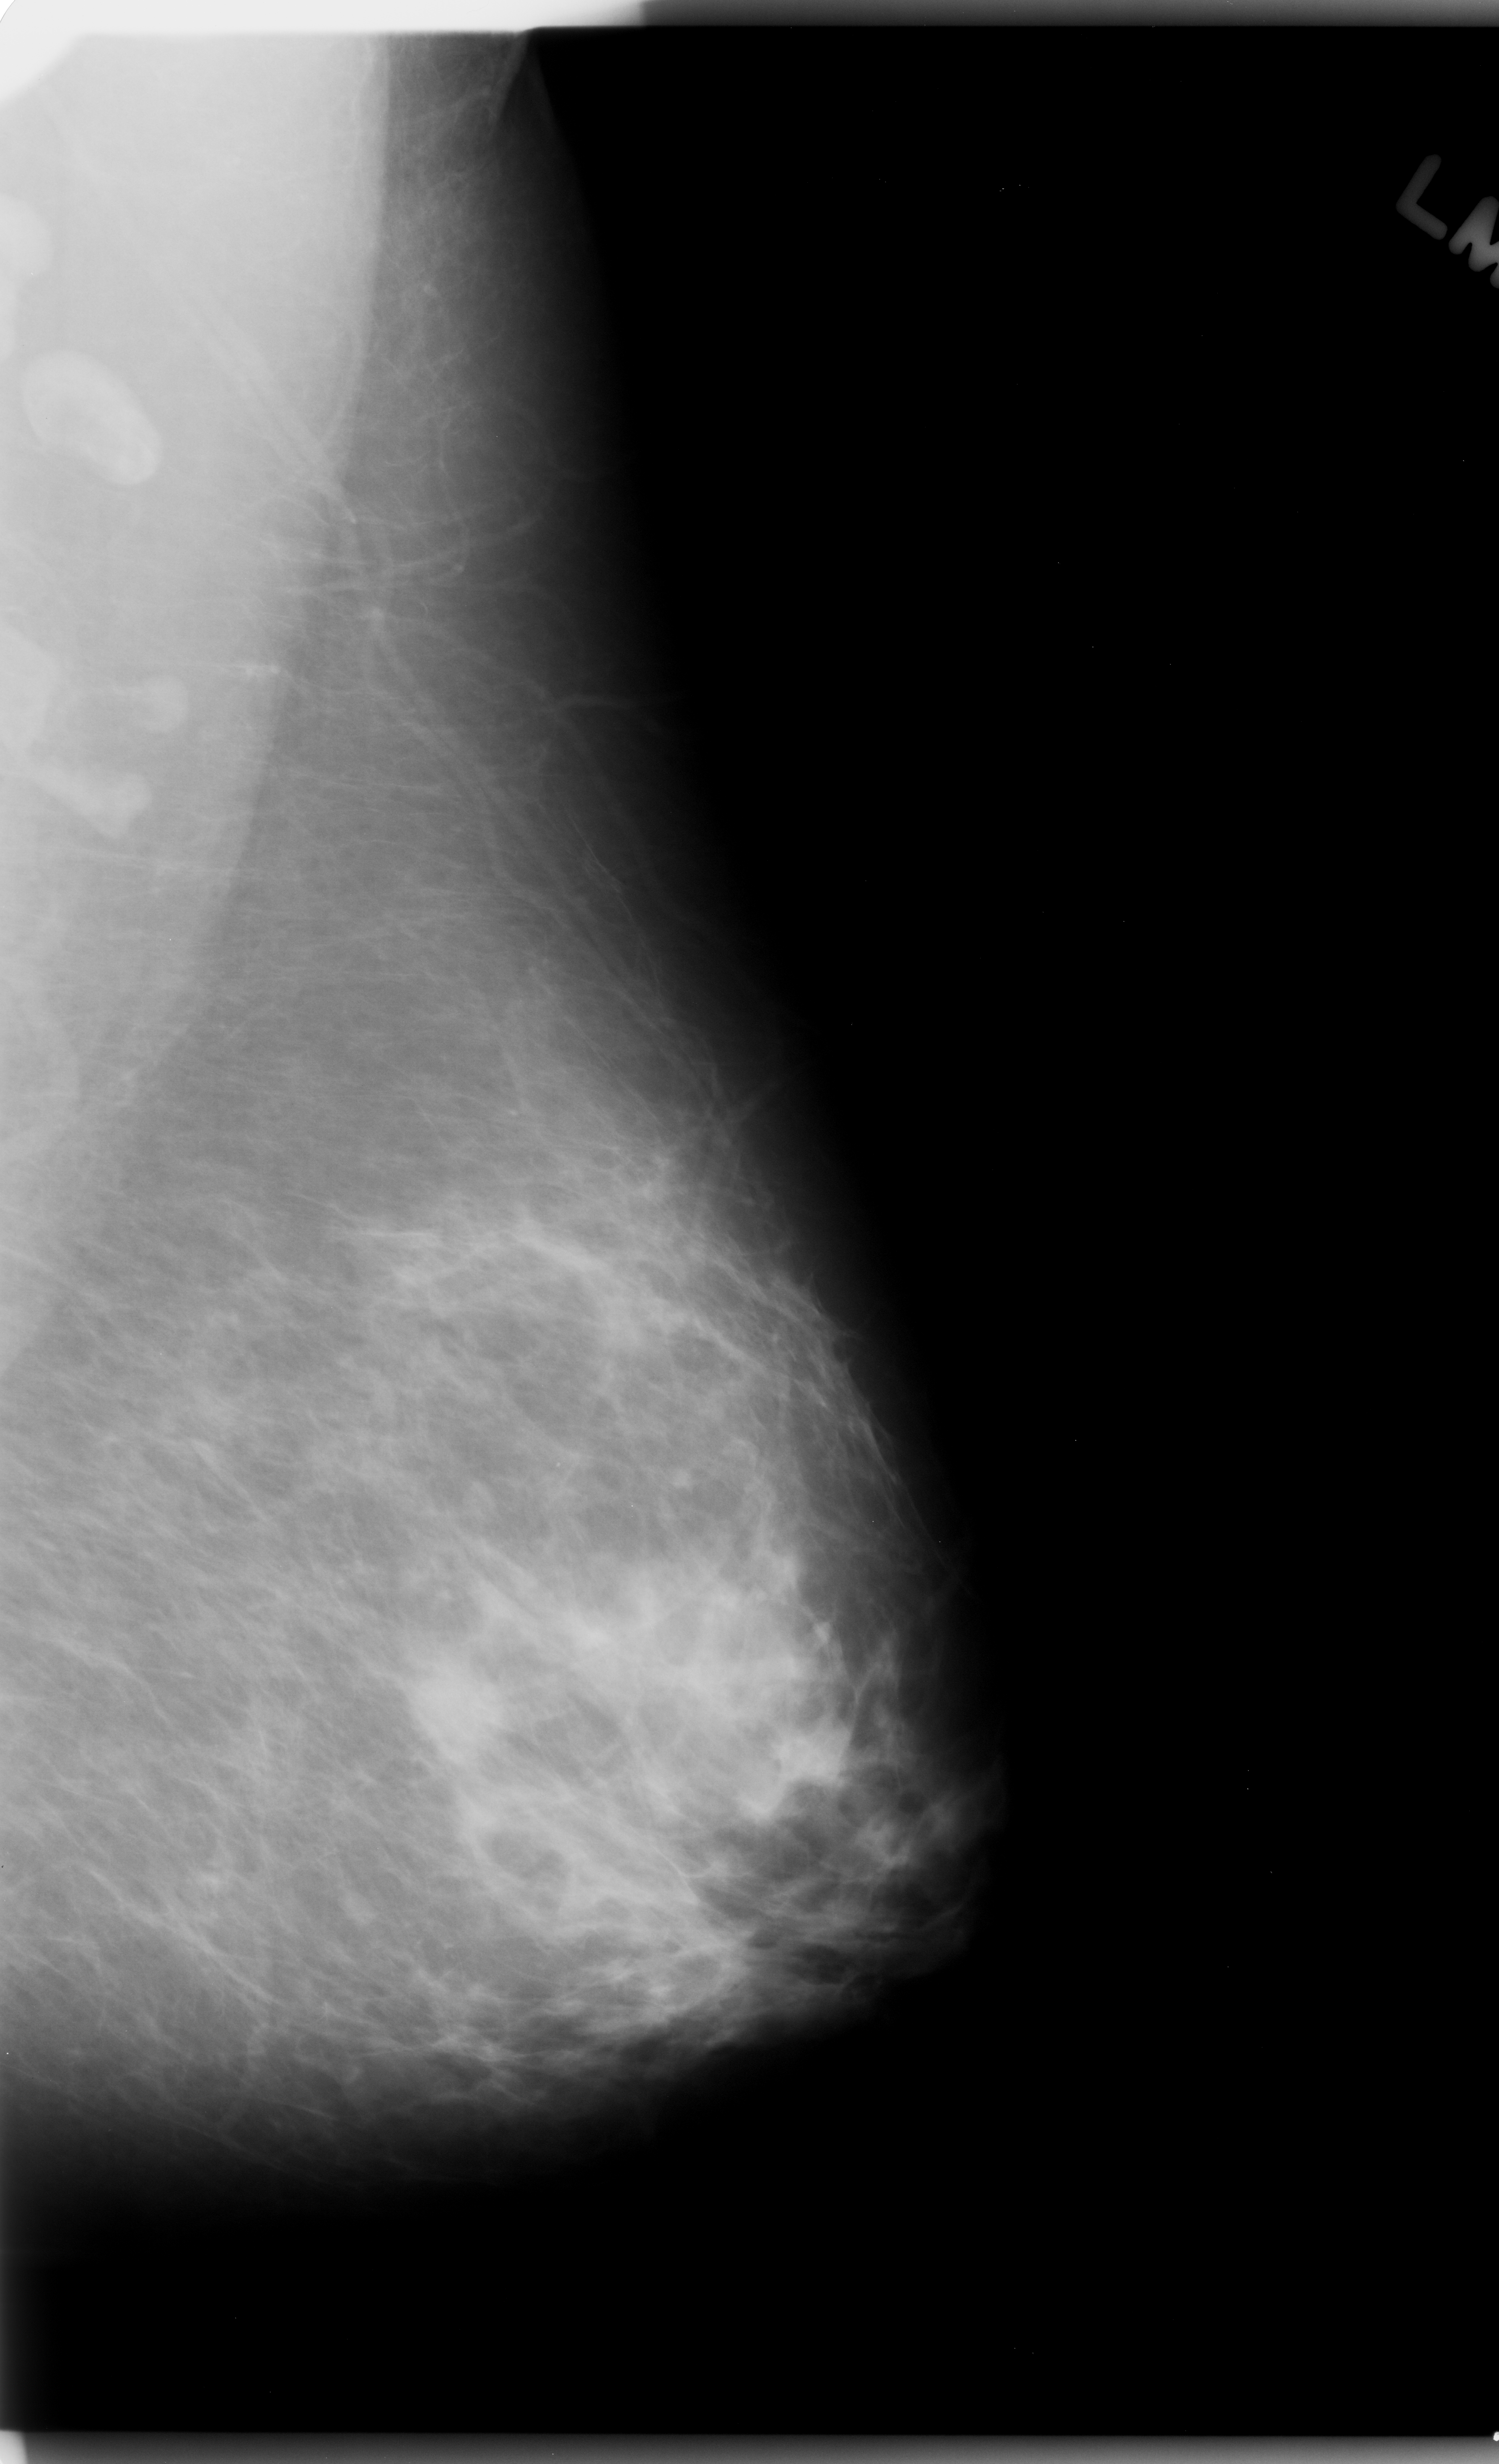
Mammogram (digitized film), left breast, mediolateral oblique (MLO) view, breast composition: scattered fibroglandular densities (BI-RADS density category 2 of 4).
- Radiologist-marked abnormalities on this image: mass, shape oval, margins microlobulated; BI-RADS assessment category 4; pathology (as recorded): malignant.